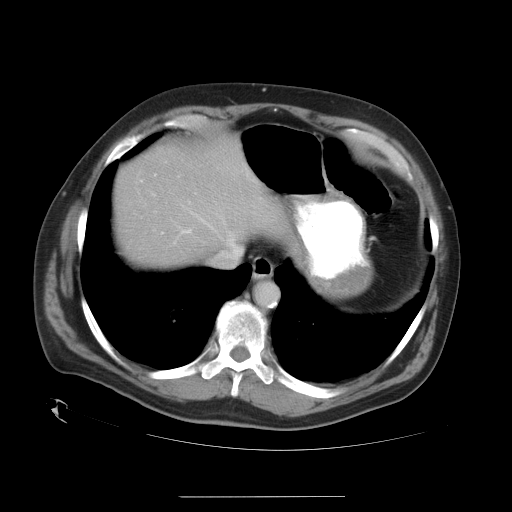
Contrast-enhanced abdominal CT, one axial slice; position 29 of 35 along the scan axis; 120 kVp; intravenous contrast given; soft-tissue window (W 400 / L 40 HU); 7.5 mm slice thickness; 512 × 512 image matrix. Male patient, age 67 years. Case-level facts recorded for this patient, not image findings: diagnosis: colorectal cancer liver metastases, imaged before liver resection; multiple liver metastases: no.
Structures marked on this image (manually delineated by an expert):
- hepatic veins: bounding box <139,173,242,258> (left, top, right, bottom; pixels)
- liver: <115,141,279,265>
- planned liver remnant (the part of the liver to remain after resection): <115,140,279,265>
- portal vein (with intrahepatic branches): <180,228,192,234>